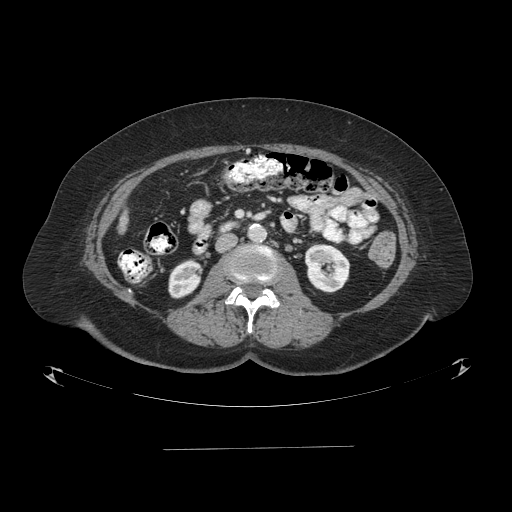
Contrast-enhanced abdominal CT (liver protocol), one axial slice; position 15 of 103 along the scan axis; reconstruction kernel STANDARD; 120 kVp; one of 2 acquisitions stored at this slice position; soft-tissue window (W 400 / L 40 HU); 2.5 mm slice thickness; 512 × 512 image matrix, field of view 500 × 500 mm. From the clinical record (not read from this slice): diagnosis: hepatocellular carcinoma (patient treated with transarterial chemoembolisation; whether this scan precedes or follows treatment is not stated here); TNM stage (as recorded): Stage-IIIA; Child-Pugh class: A; tumour differentiation: poorly differentiated; tumour nodularity: multinodular.
Outlined on this slice (semi-automatically segmented with operator editing):
- liver parenchyma outside the tumour (the mass and vessels are separate outlines, so this box may not span the whole liver): bounding box [x1, y1, x2, y2] px = [118, 212, 128, 233]